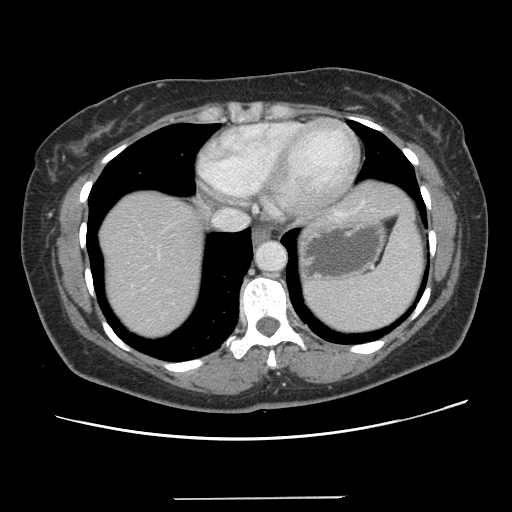
Contrast-enhanced abdominal CT, one axial slice. Slice 120 of 141 in the series (ordered by position). Soft-tissue window (W 400 / L 40 HU). 512 × 512 image matrix, field of view 366 × 366 mm. Female patient, age 53 years. From the clinical record (not read from this slice): diagnosis: colorectal cancer liver metastases, imaged before liver resection; multiple liver metastases: no; largest metastasis: 14.5 cm; disease in both lobes: yes.
Annotated regions visible in this slice (expert manual segmentation):
- hepatic veins: bounding box [x1, y1, x2, y2] px = [142, 209, 244, 278]
- liver: [98, 181, 410, 339]
- planned liver remnant (the part of the liver to remain after resection): [98, 214, 205, 339]